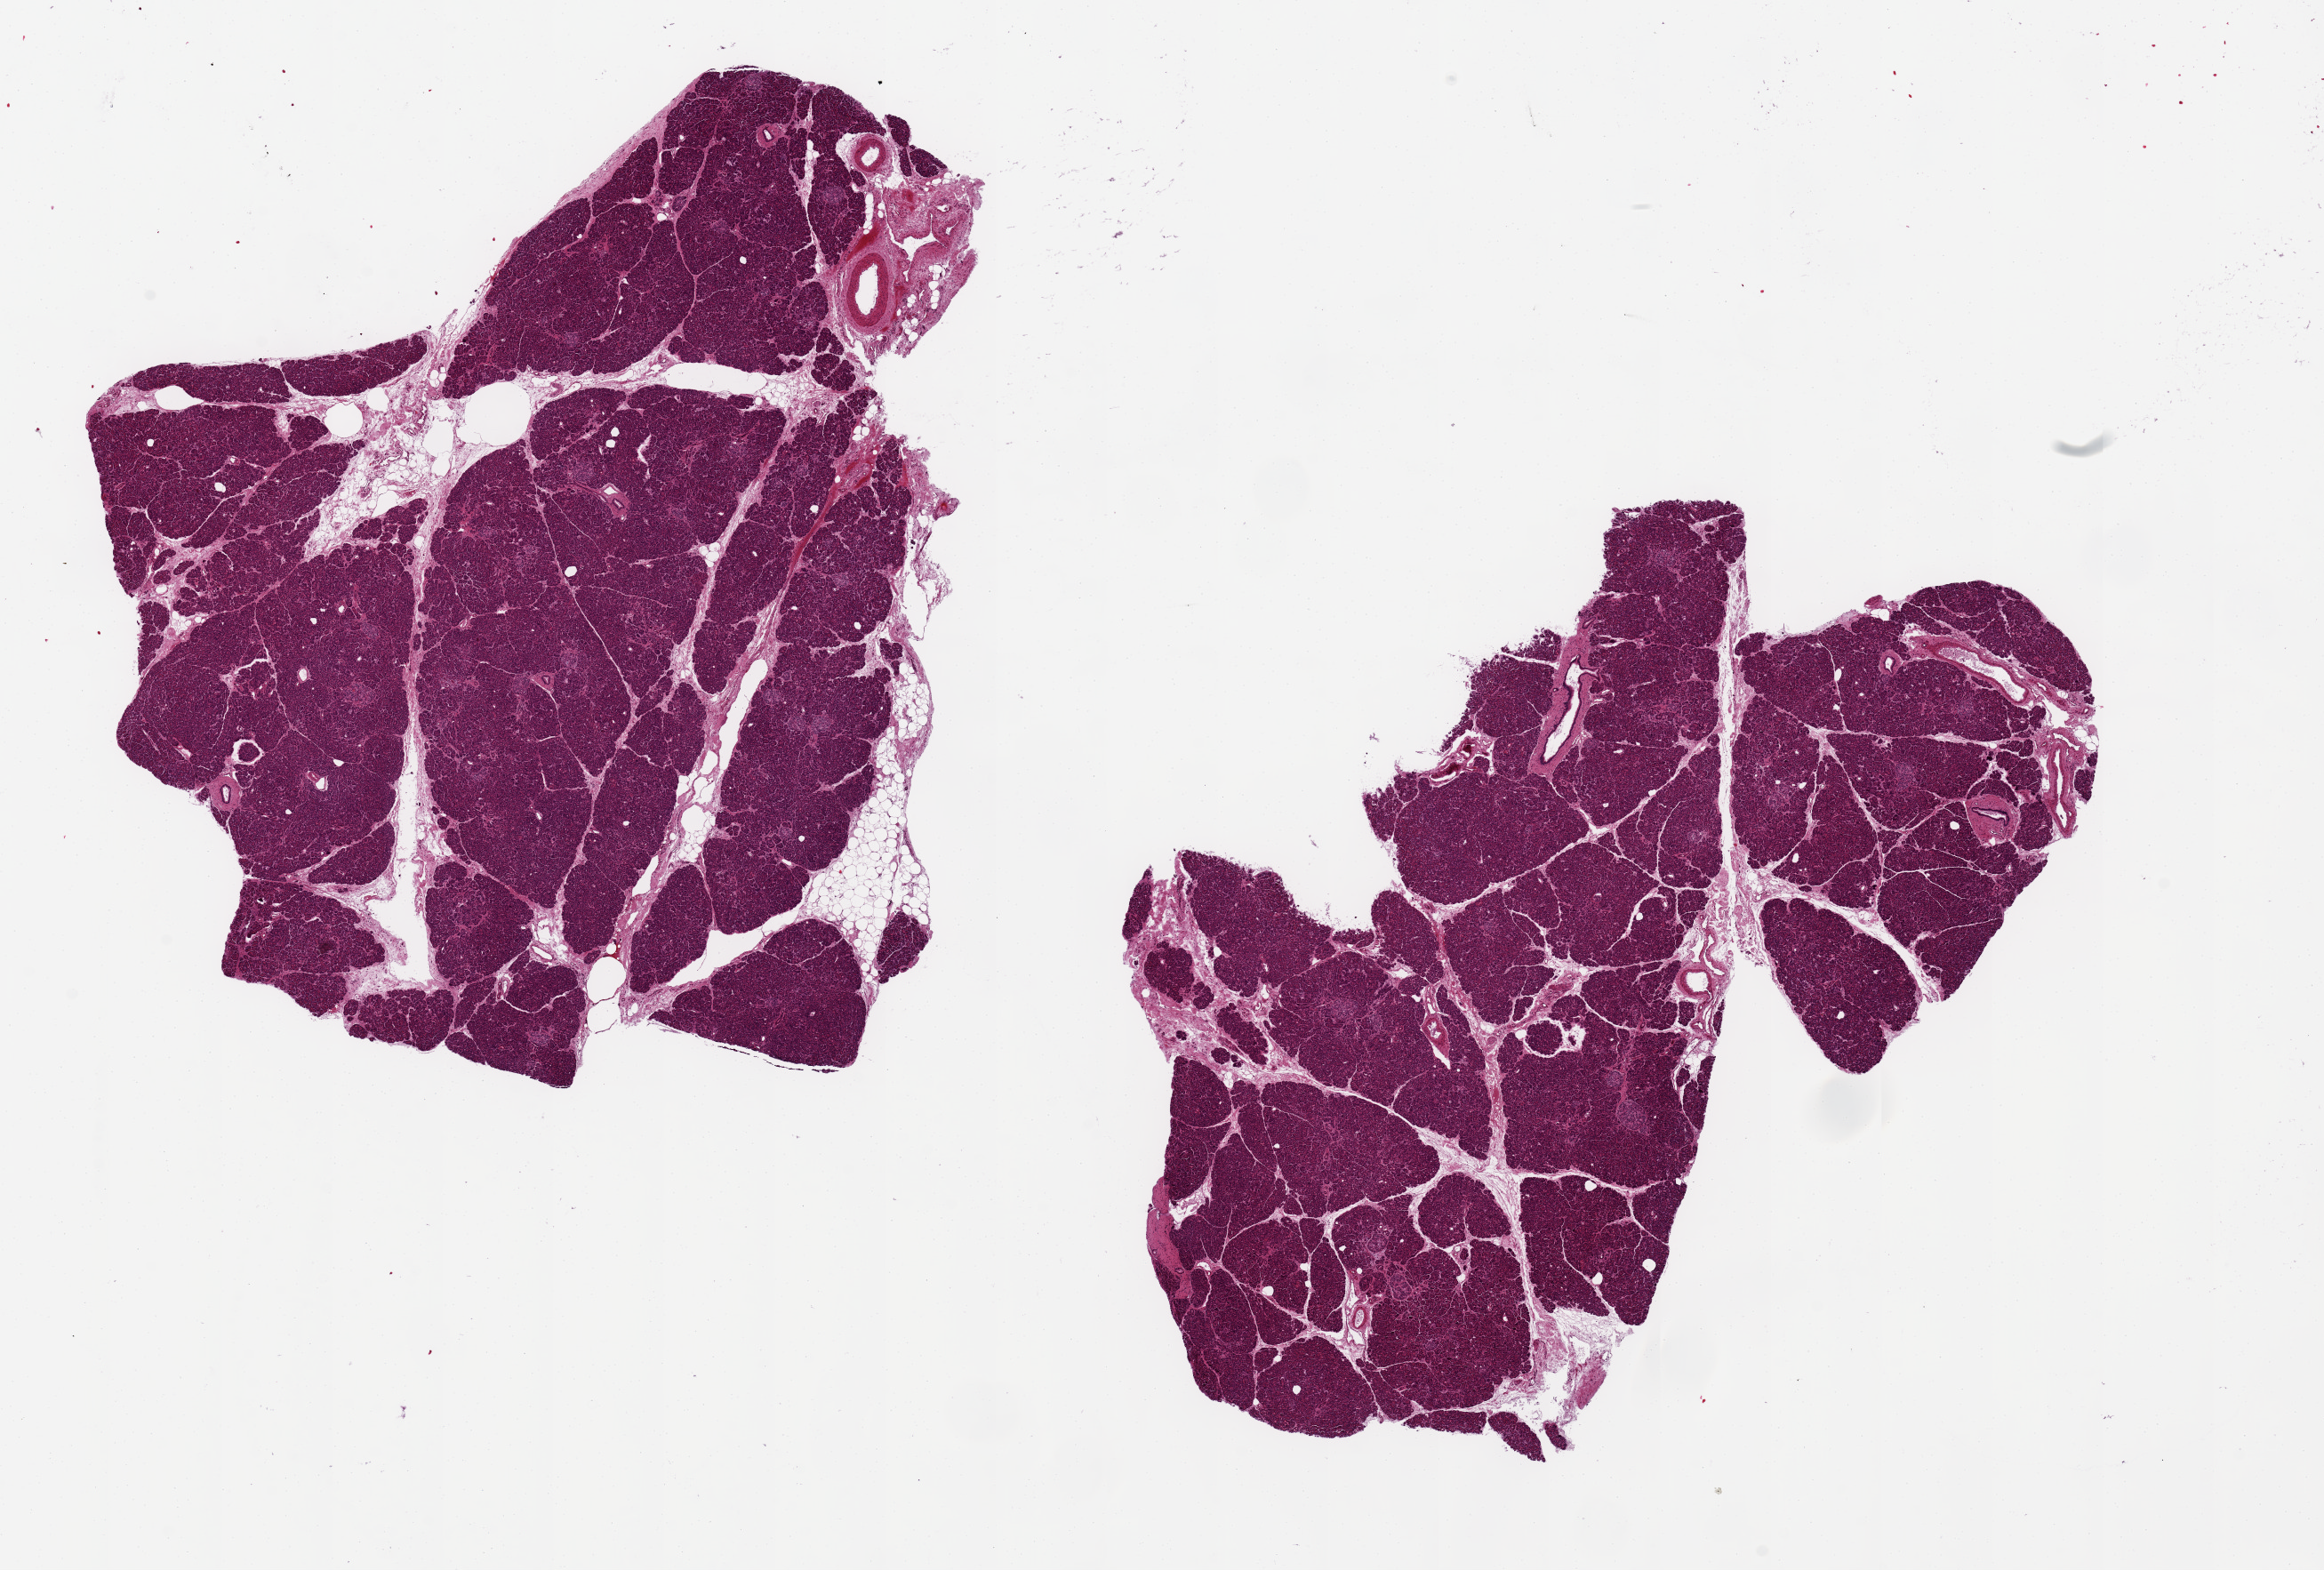
Digitized H&E-stained section, whole scanned area (about 20.7 x 14.0 mm, slide scanned at 20x) shown as a low-resolution overview, PAXgene-fixed, paraffin-embedded tissue, target tissue: pancreas, tissue donor sample. Female donor.
* review note (as recorded): 2 aliquots, ~8x6mm